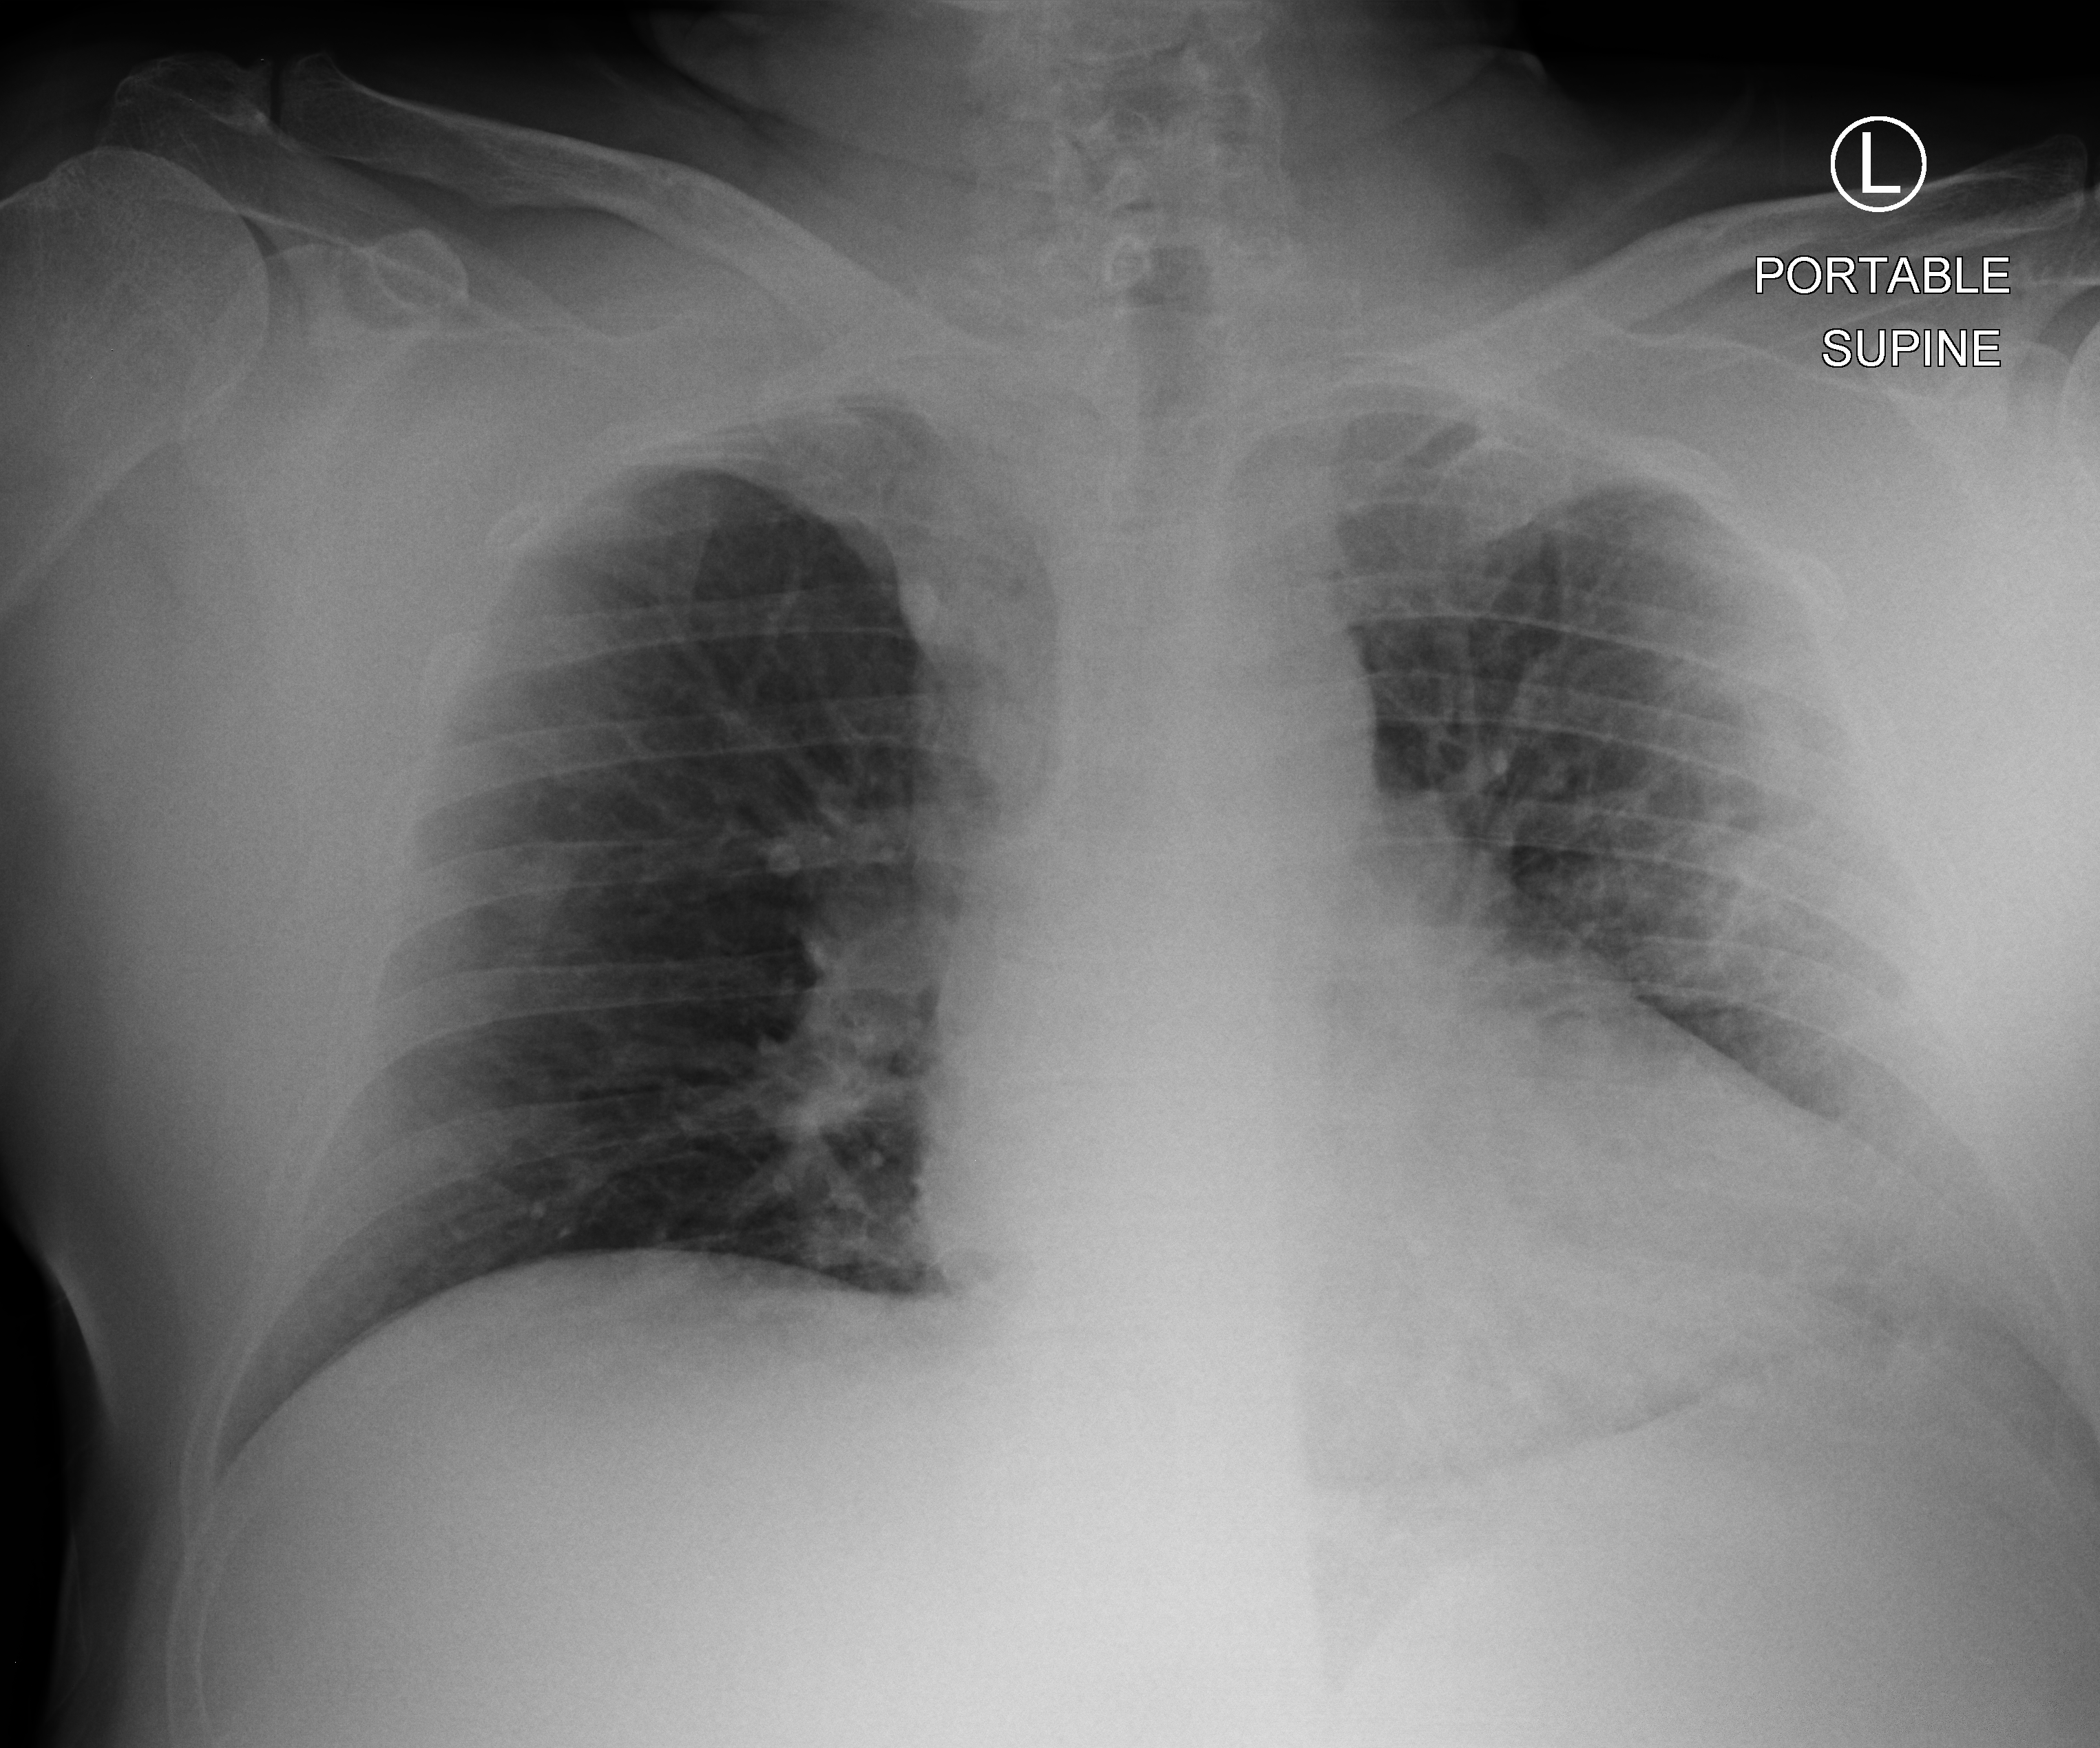
Bedside chest radiograph (computed radiography), anteroposterior (AP) projection. Male patient hospitalised with COVID-19, age 60–74 years.
From the hospital-stay record, not from the radiograph (when in the stay this image was taken is not recorded): length of hospital stay: 5 days; mechanically ventilated during this hospital stay: no.